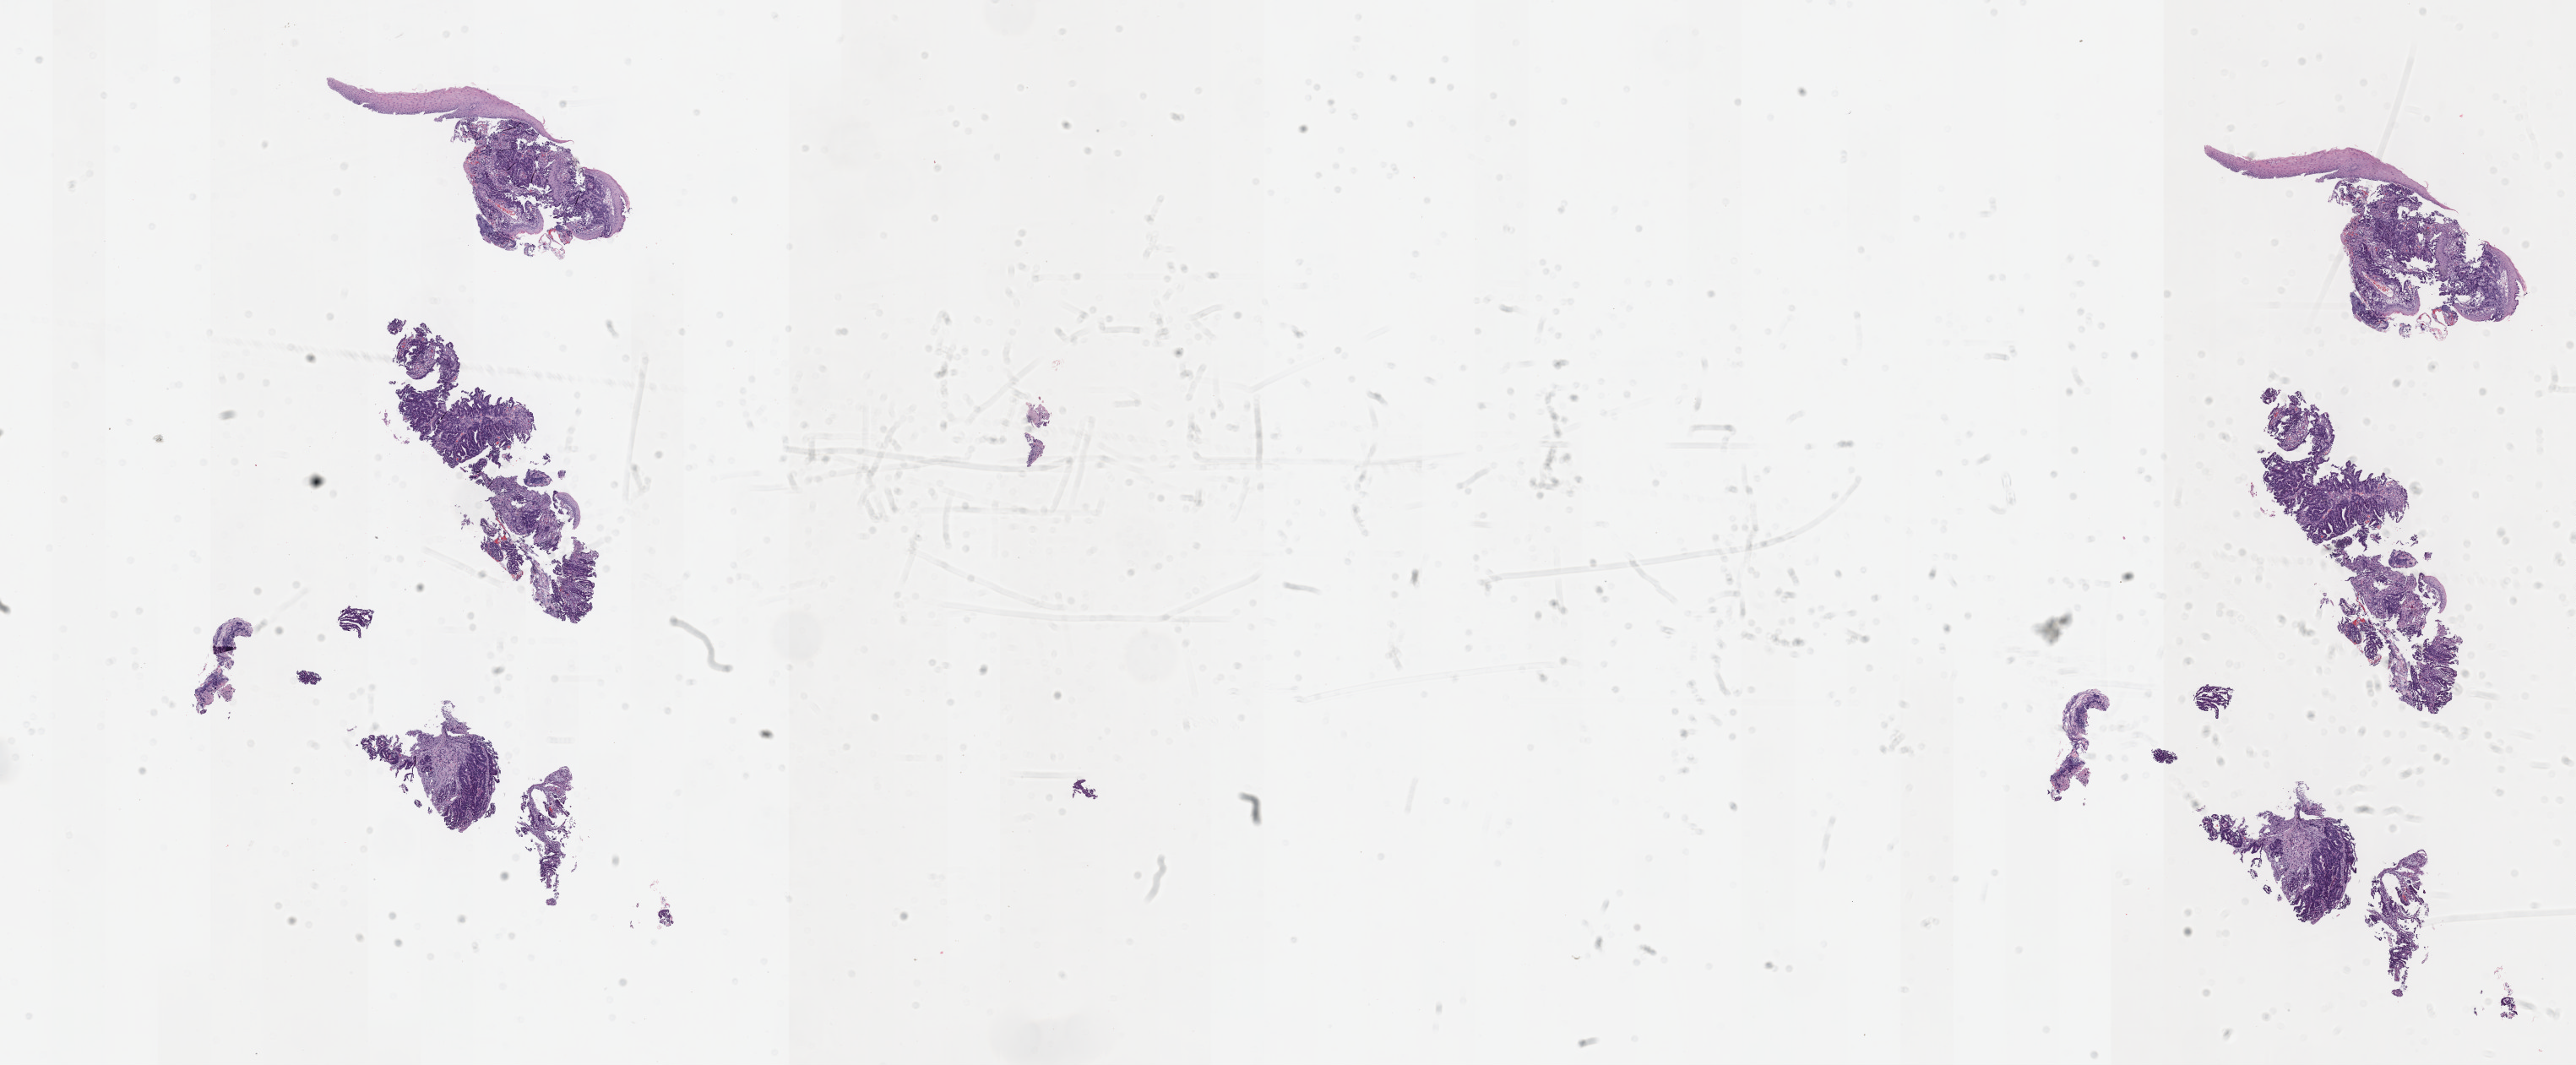
H&E whole-slide image, a low-resolution overview of the entire scanned area, about 24.7 x 10.2 mm (acquisition: 40x scan). Formalin-fixed paraffin-embedded (FFPE) diagnostic section. Primary tumour sample from the esophagus. Patient: male, age at initial diagnosis 72 years. Histologic grade: G2 (moderately differentiated).
- histologic diagnosis: Adenocarcinoma, NOS (lower third of esophagus)